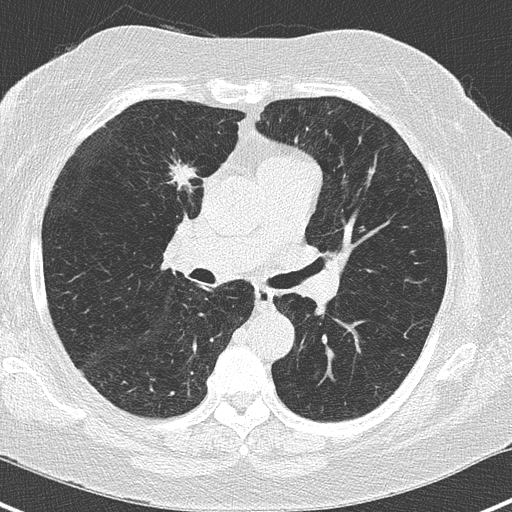
Low-dose screening chest CT, axial slice; third annual screen; lung window (W 1500 / L -600 HU); 2 mm slice thickness; lung (sharp) reconstruction kernel (B50f); 512 × 512 image matrix, field of view 303 × 303 mm. Female participant, aged 62 years at enrolment. Current smoker at enrolment.
- Lesion marked by an expert reader, bounding box <145,146,213,209> (left, top, right, bottom; pixels).
- The screening reader recorded 4 non-calcified nodules or masses ≥4 mm on this exam (right upper lobe, left lower lobe, left lower lobe); which of them this box marks is not recorded.
- Lung cancer was diagnosed 41 days after this screen: adenocarcinoma, NOS, right upper lobe, moderately differentiated (G2), stage IA (AJCC 6th edition), 15 mm at pathology.